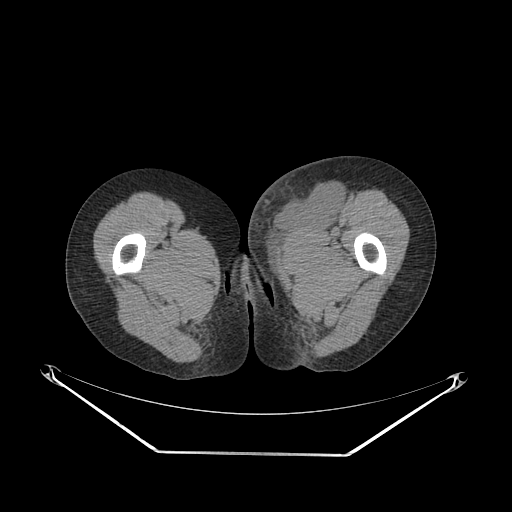
CT of an extremity soft-tissue mass (from a PET/CT study), one axial slice; reconstruction kernel SOFT; soft-tissue window (W 400 / L 40 HU); 3.75 mm slice thickness; 512 × 512 image matrix, field of view 500 × 500 mm. Female patient. From the clinical record (not read from this slice): histological type: leiomyosarcoma; grade: high; site of the primary tumour: groin.
Structures marked on this image (expert contour drawn on MRI and transferred to this co-registered scan by the dataset authors):
- gross tumour volume including surrounding oedema: bounding box (x1, y1, x2, y2) in pixels: (247, 174, 343, 250)
- gross tumour volume (mass): (272, 185, 343, 227)